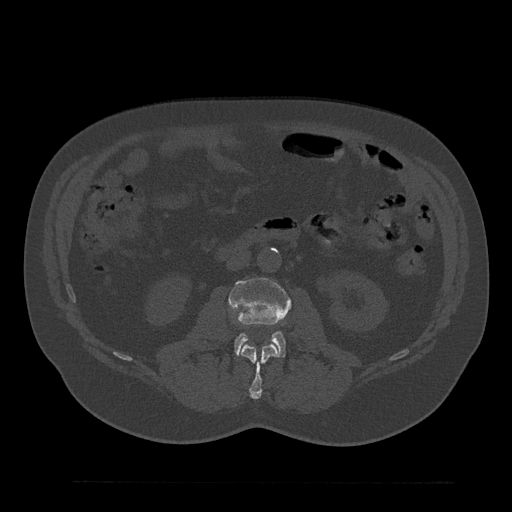
CT including the spine, one axial slice. 120 kVp. Bone window (W 1800 / L 400 HU). 0.5 mm slice thickness. 512 × 512 image matrix, field of view 430 × 430 mm. Male patient, age 61 years. Case-level facts recorded for this patient, not image findings: primary cancer: prostate.
Outlined on this slice (semi-automatically segmented with operator editing):
- L2 vertebra: box from (x=241, y=344) to (x=278, y=399) px
- L3 vertebra: (x=230, y=277)–(x=292, y=357)